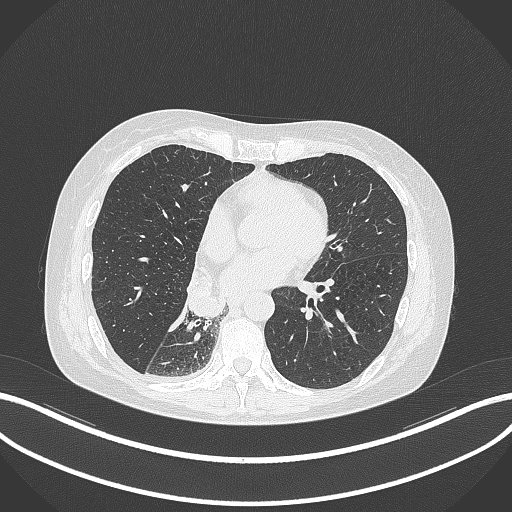
Chest CT, one axial slice. Slice 128 of 329 in the series (ordered by position). 120 kVp. Lung window (W 1500 / L -600 HU). 1 mm slice thickness. 512 × 512 image matrix, field of view 400 × 400 mm. Patient: female, 63 years. Case-level facts recorded for this patient, not image findings: clinical TNM (as recorded): T1c N0 M0.
Structures marked on this image (bounding box drawn by a radiologist):
- lung tumour (recorded histology: adenocarcinoma): box from (x=183, y=262) to (x=227, y=322) px